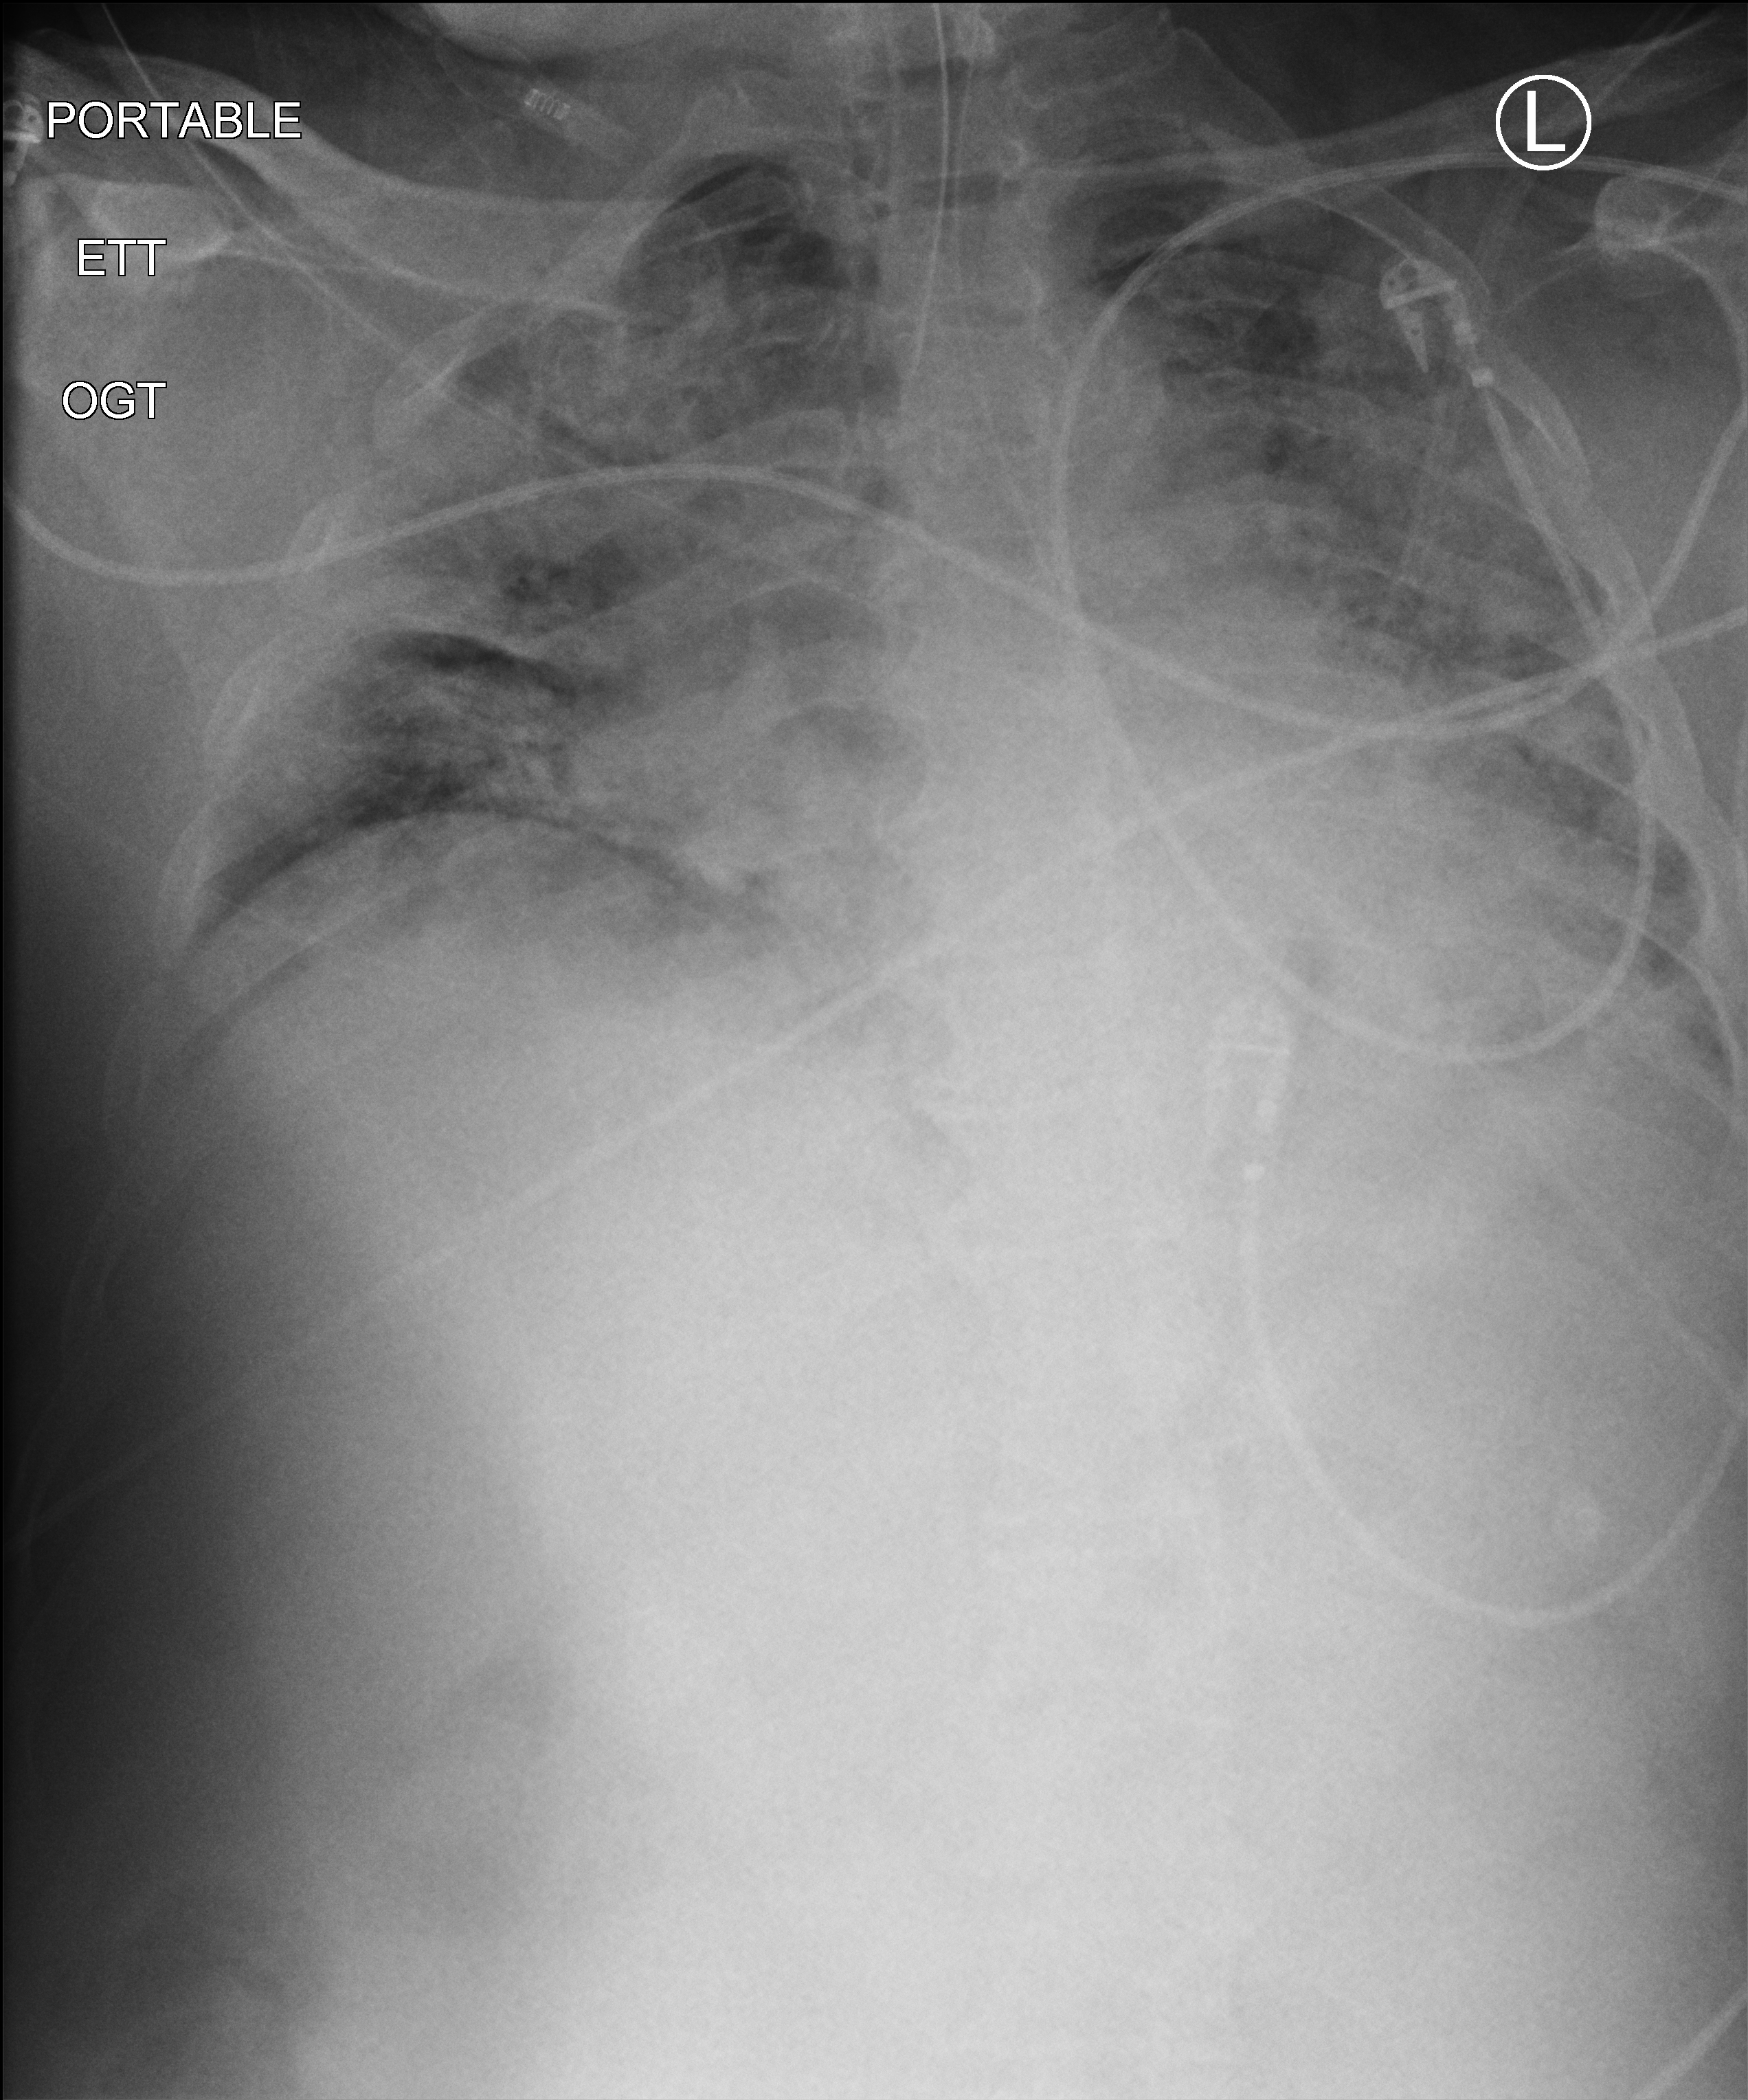
Chest X-ray (portable). Patient hospitalised with COVID-19; male, aged 60–74 years.
Admission-level facts for this patient (not findings on this image; timing relative to this image not recorded): mechanically ventilated during this hospital stay: yes; chronic kidney disease (admission record): no; admitted to intensive care during this hospital stay: yes.